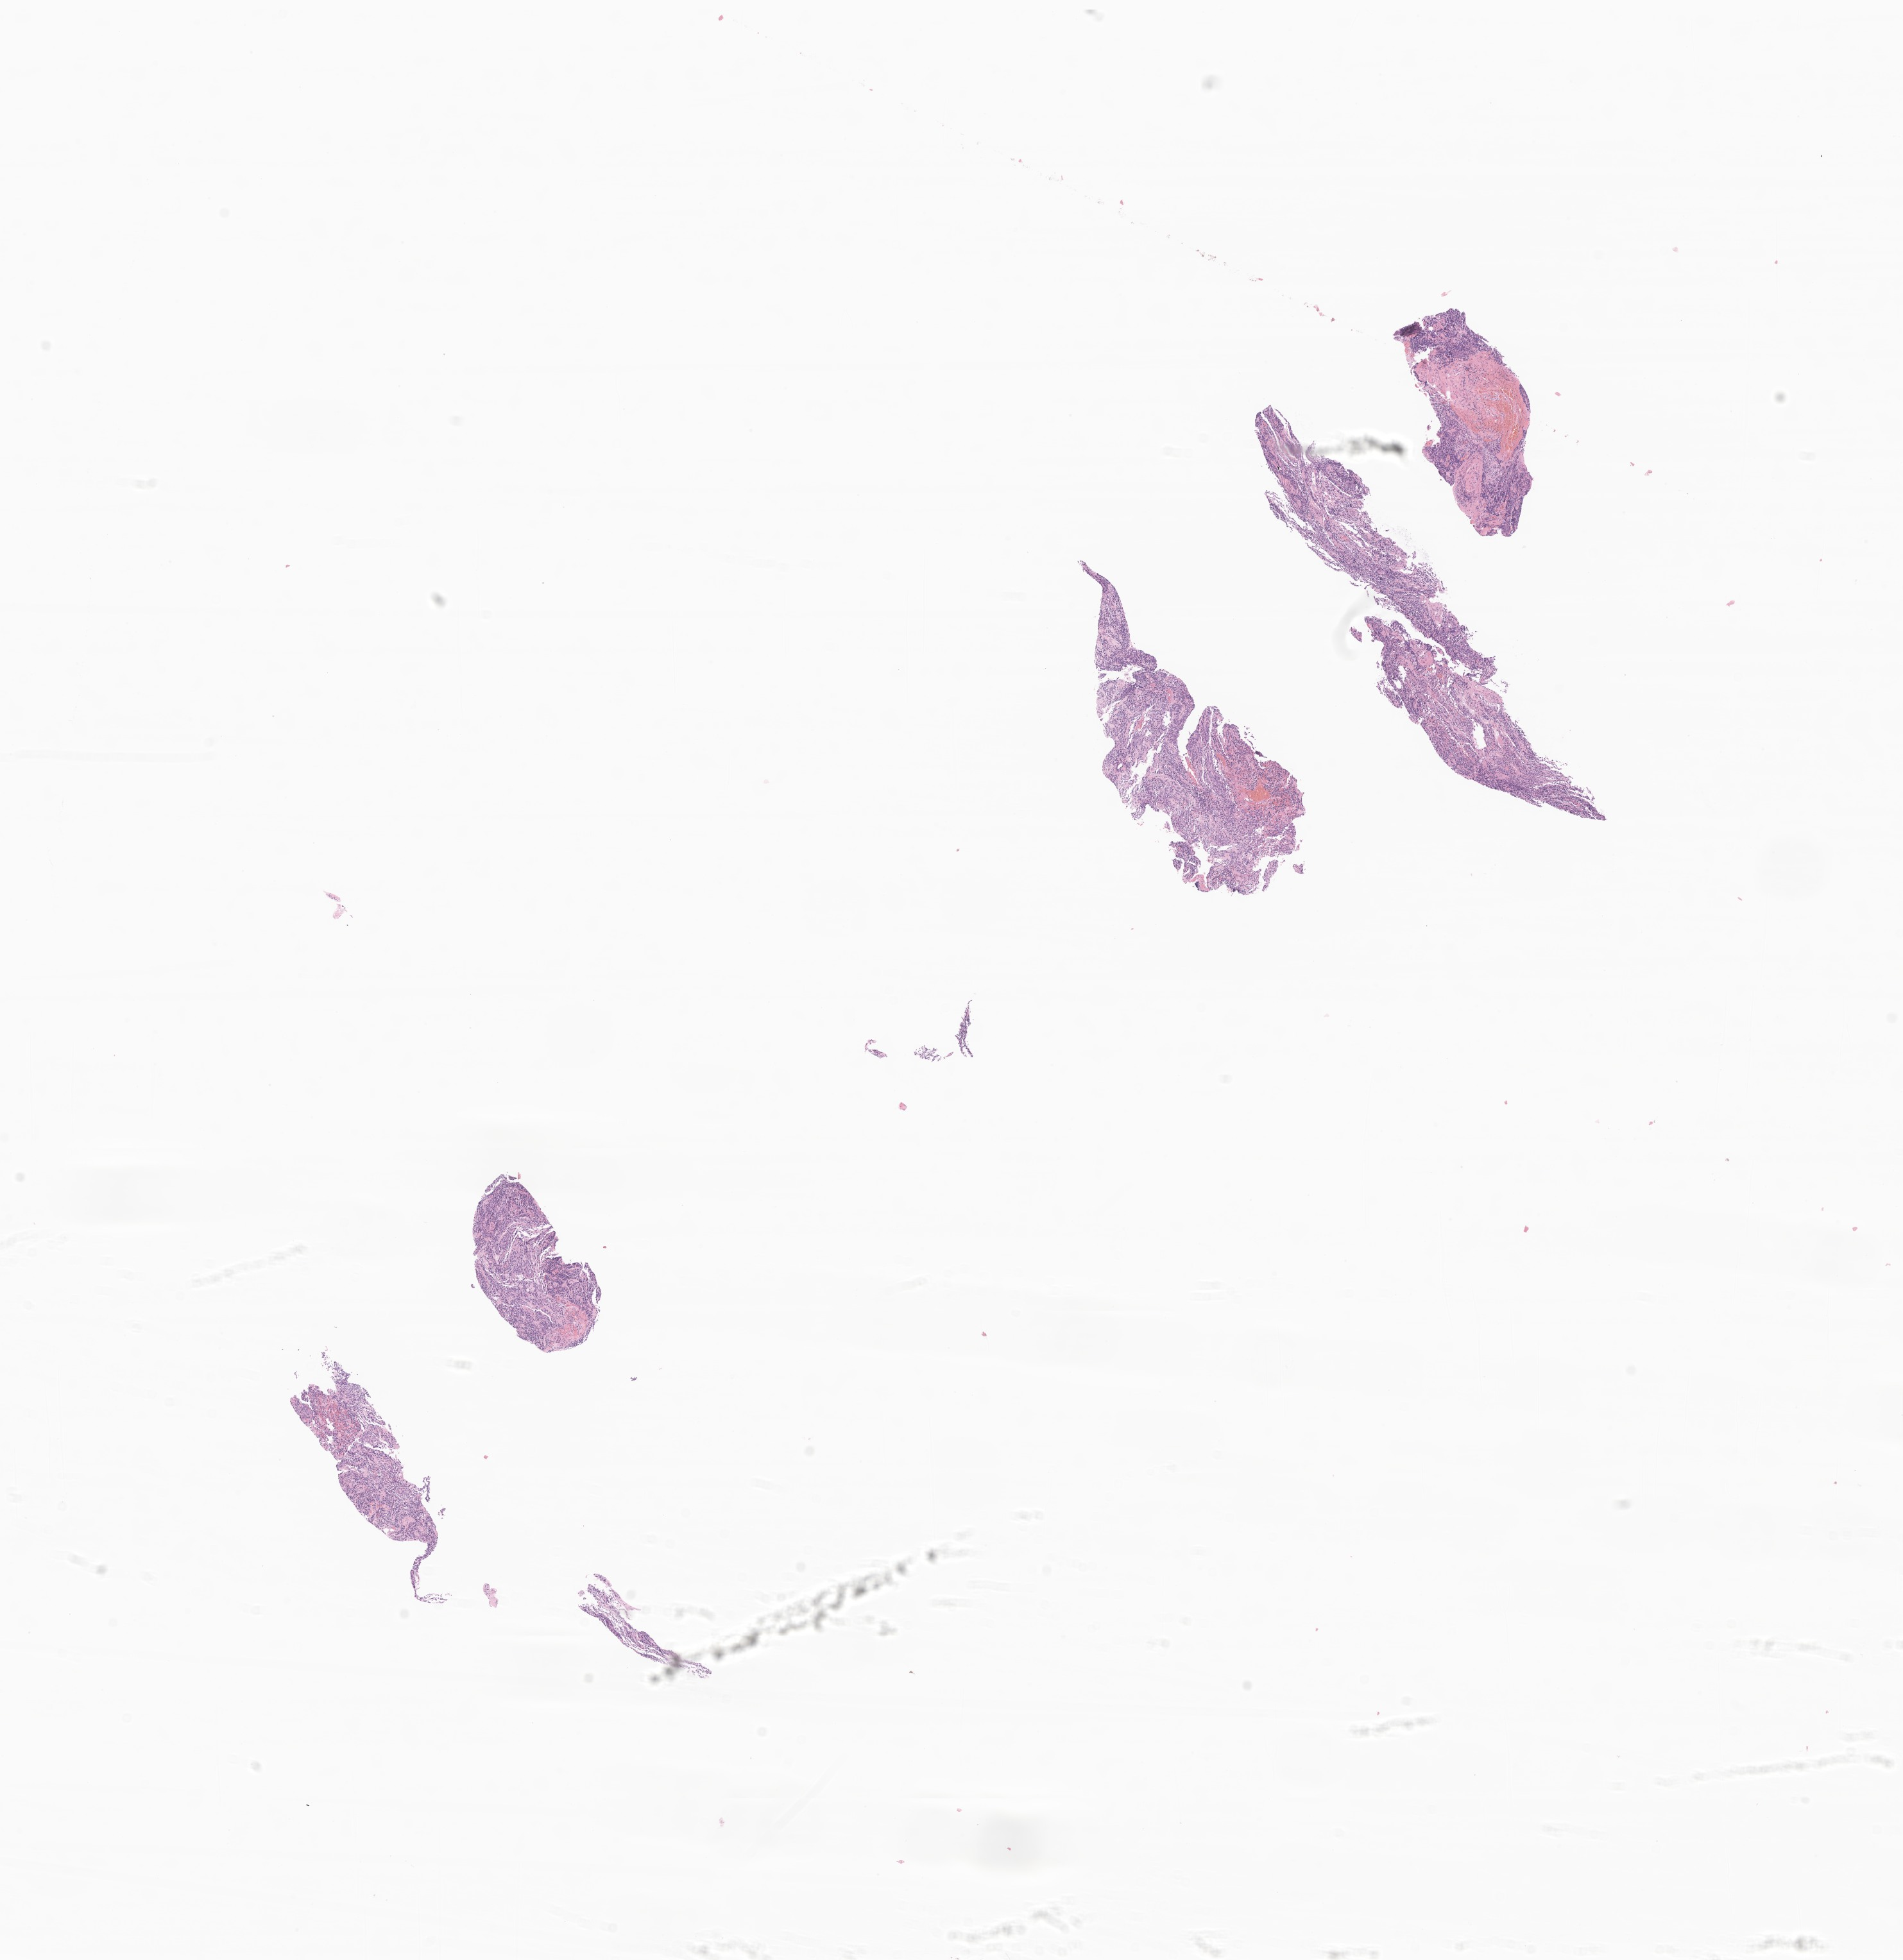
Digitized H&E-stained section of tumor tissue from the spinal cord, a low-resolution overview of the entire scanned area, about 12.5 x 12.9 mm. Formalin-fixed, paraffin-embedded (FFPE) tissue. Patient: female, age 225 months (18 years 9 months).
- diagnosis: Neoplasm, uncertain whether benign or malignant